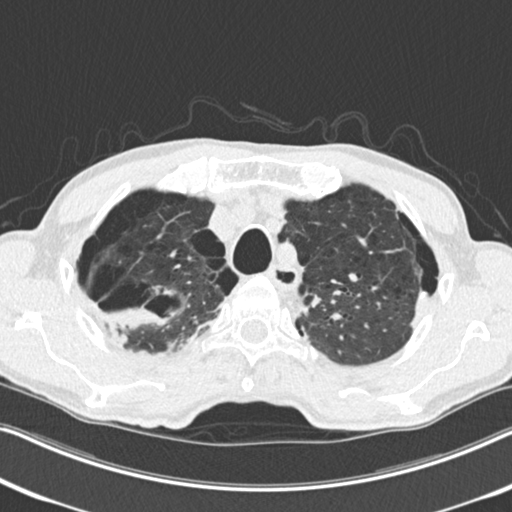
Low-dose screening chest CT, one axial slice; slice 204 of 251 in the series (ordered by position); reconstruction kernel B30f; 120 kVp; lung window (W 1500 / L -600 HU); 2 mm slice thickness; 512 × 512 image matrix, field of view 334 × 334 mm.
Annotated regions visible in this slice (expert manual segmentation):
- lesion 1 (tumor, upper lobe of right lung): box from (x=104, y=307) to (x=167, y=330) px